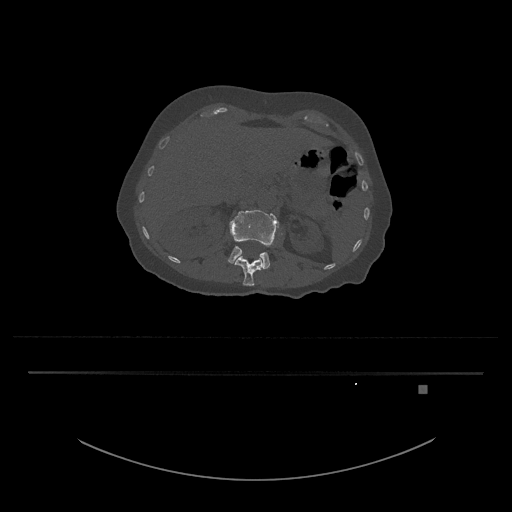
CT including the spine, one axial slice; position 523 of 797 along the scan axis; bone window (W 1800 / L 400 HU); 0.5 mm slice thickness; 512 × 512 image matrix. Patient: female, 57 years. From the clinical record (not read from this slice): primary cancer: cervical.
Annotated regions visible in this slice (semi-automatically segmented with operator editing):
- L1 vertebra: box from (x=234, y=255) to (x=263, y=286) px